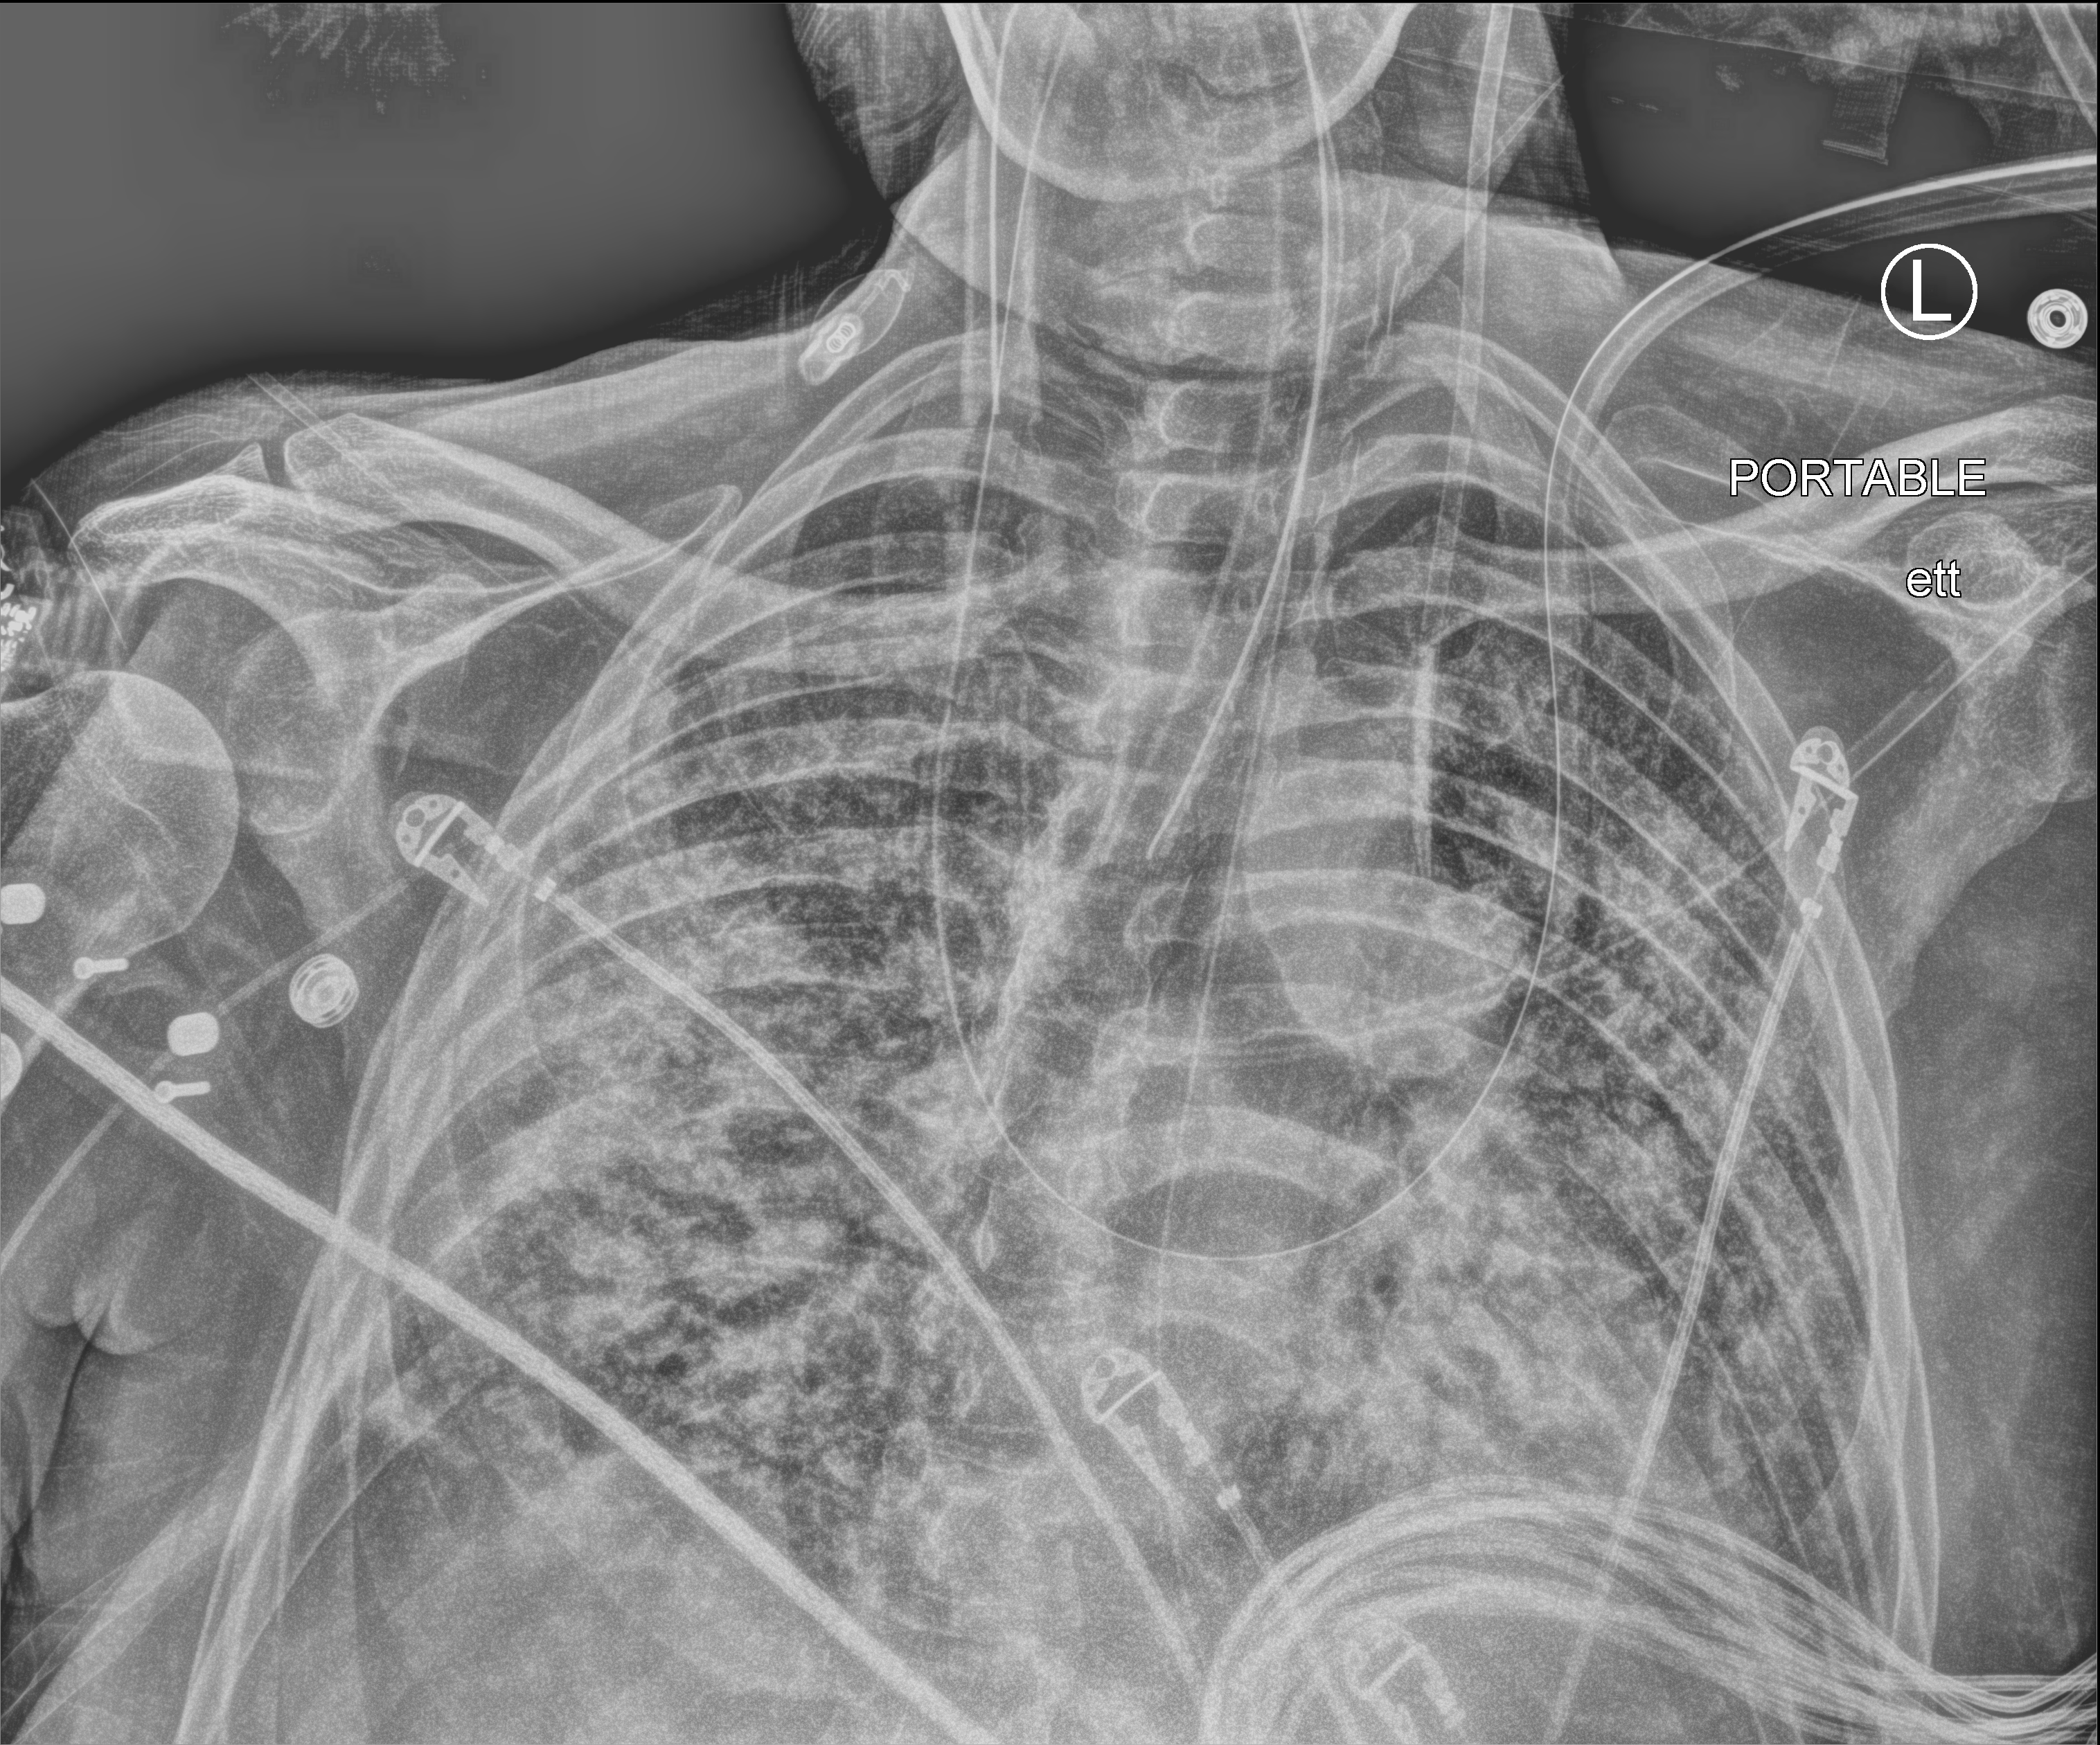
Chest X-ray (portable). Male patient hospitalised with COVID-19, age 18–59 years.
Admission-level facts for this patient (not findings on this image; timing relative to this image not recorded):
- admitted to intensive care during this hospital stay: yes